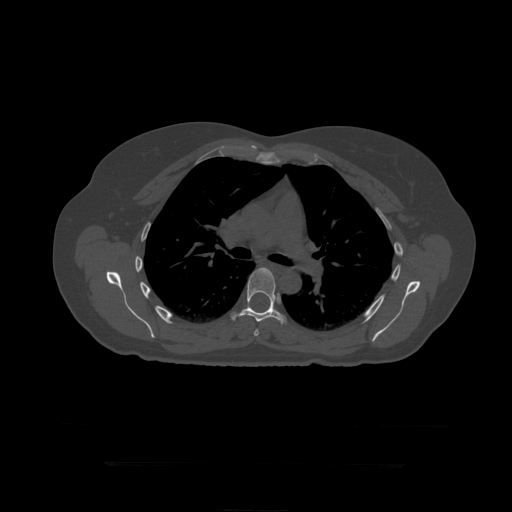
CT including the spine, one axial slice; slice 304 of 399 in the series (ordered by position); bone window (W 1800 / L 400 HU); 512 × 512 image matrix, field of view 450 × 450 mm. Patient age 41 years. Case-level facts recorded for this patient, not image findings: primary cancer: breast.
Structures marked on this image (semi-automatic segmentation, software-assisted and operator-edited):
- T6 vertebra: bounding box [x1, y1, x2, y2] px = [254, 329, 259, 336]
- T7 vertebra: [231, 268, 287, 325]